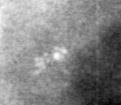
Crop from a digitized film mammogram around one marked abnormality, left breast, CC view, BI-RADS breast density category 4 (scale 1–4).
- Marked abnormality: calcifications, morphology pleomorphic, distribution clustered; BI-RADS assessment category 4; pathology (as recorded): benign.